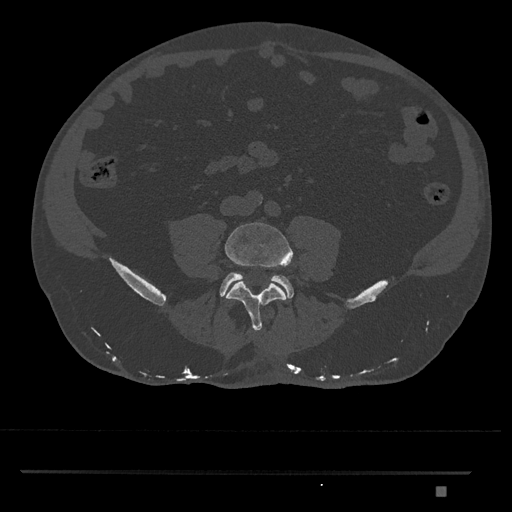
CT including the spine, one axial slice; slice 594 of 1134 in the series (ordered by position); reconstruction kernel Br40s/3; bone window (W 1800 / L 400 HU); 0.5 mm slice thickness; 512 × 512 image matrix, field of view 429 × 429 mm. Patient: male, 65 years. From the clinical record (not read from this slice): primary cancer: prostate.
Outlined on this slice (semi-automatic segmentation, software-assisted and operator-edited):
- L4 vertebra: bounding box [x1, y1, x2, y2] px = [225, 222, 293, 332]
- L5 vertebra: [220, 272, 294, 298]